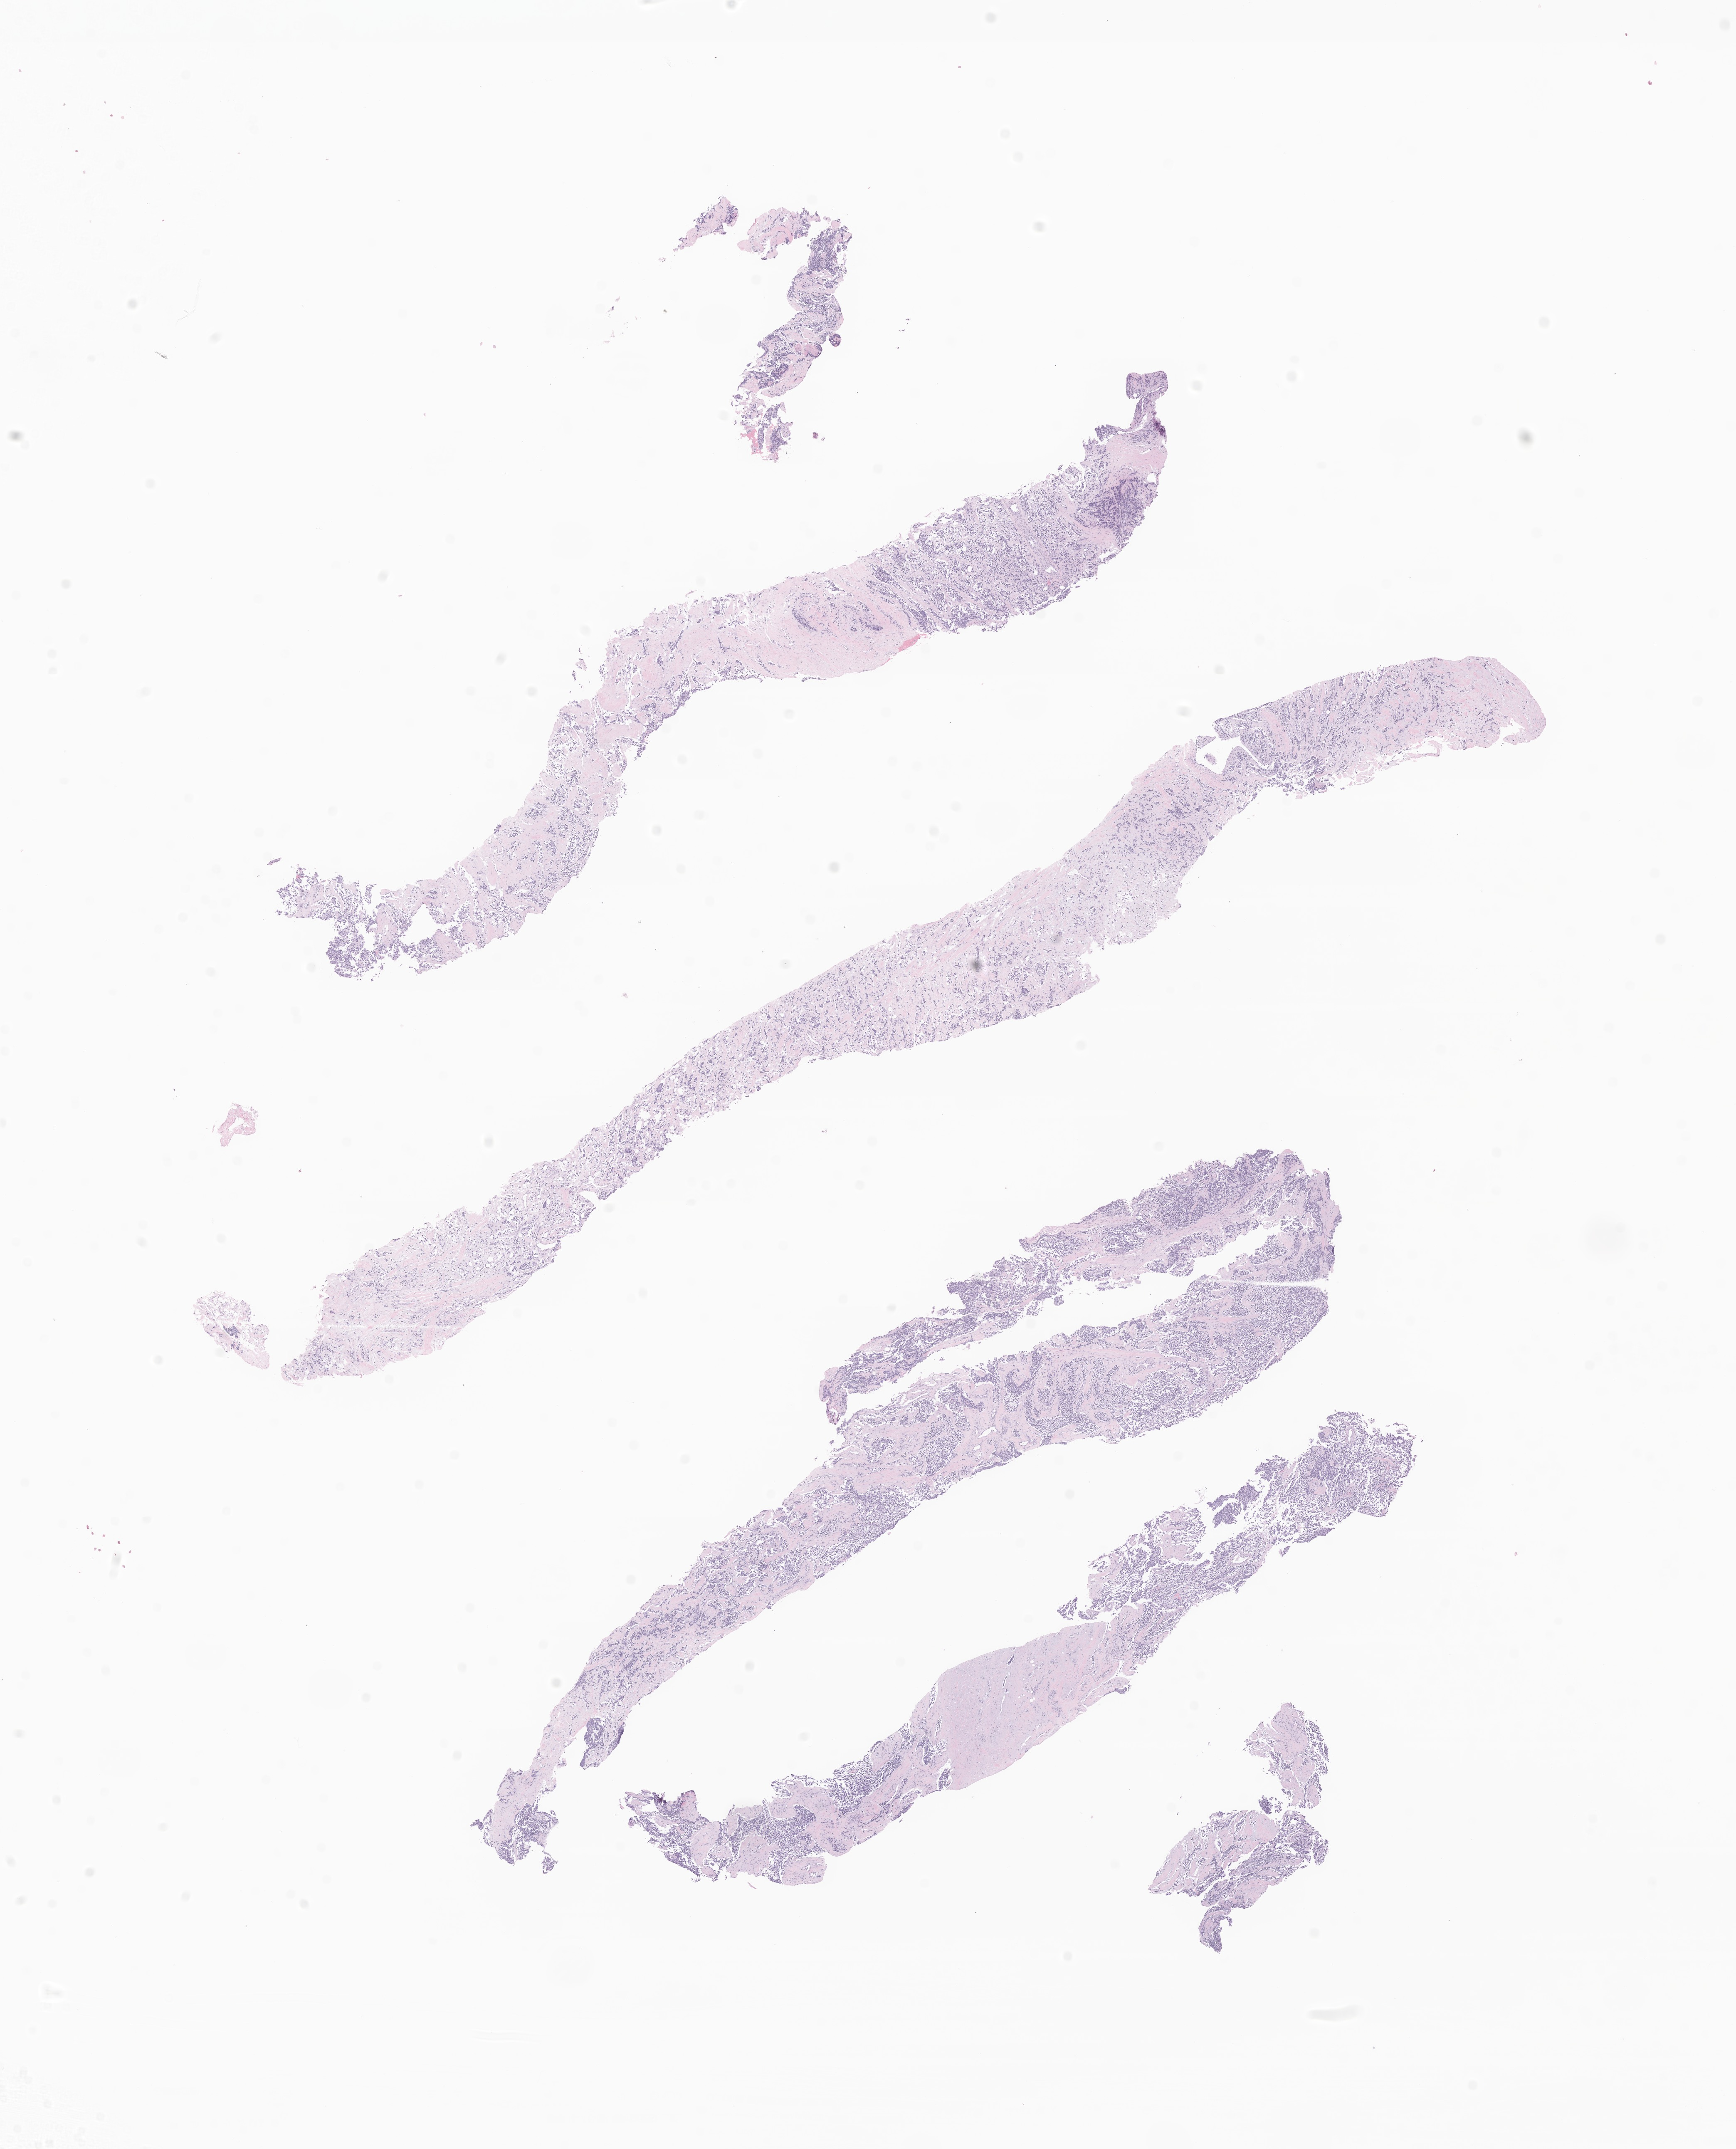
Hematoxylin and eosin (H&E) whole-slide image of tumor tissue from the soft tissue, a low-resolution overview of the entire scanned area, about 17.6 x 21.8 mm, formalin-fixed paraffin-embedded section. Female patient, age 179 months (14 years 11 months).
- diagnosis (ICD-O-3 morphology term): Rhabdomyosarcoma, NOS